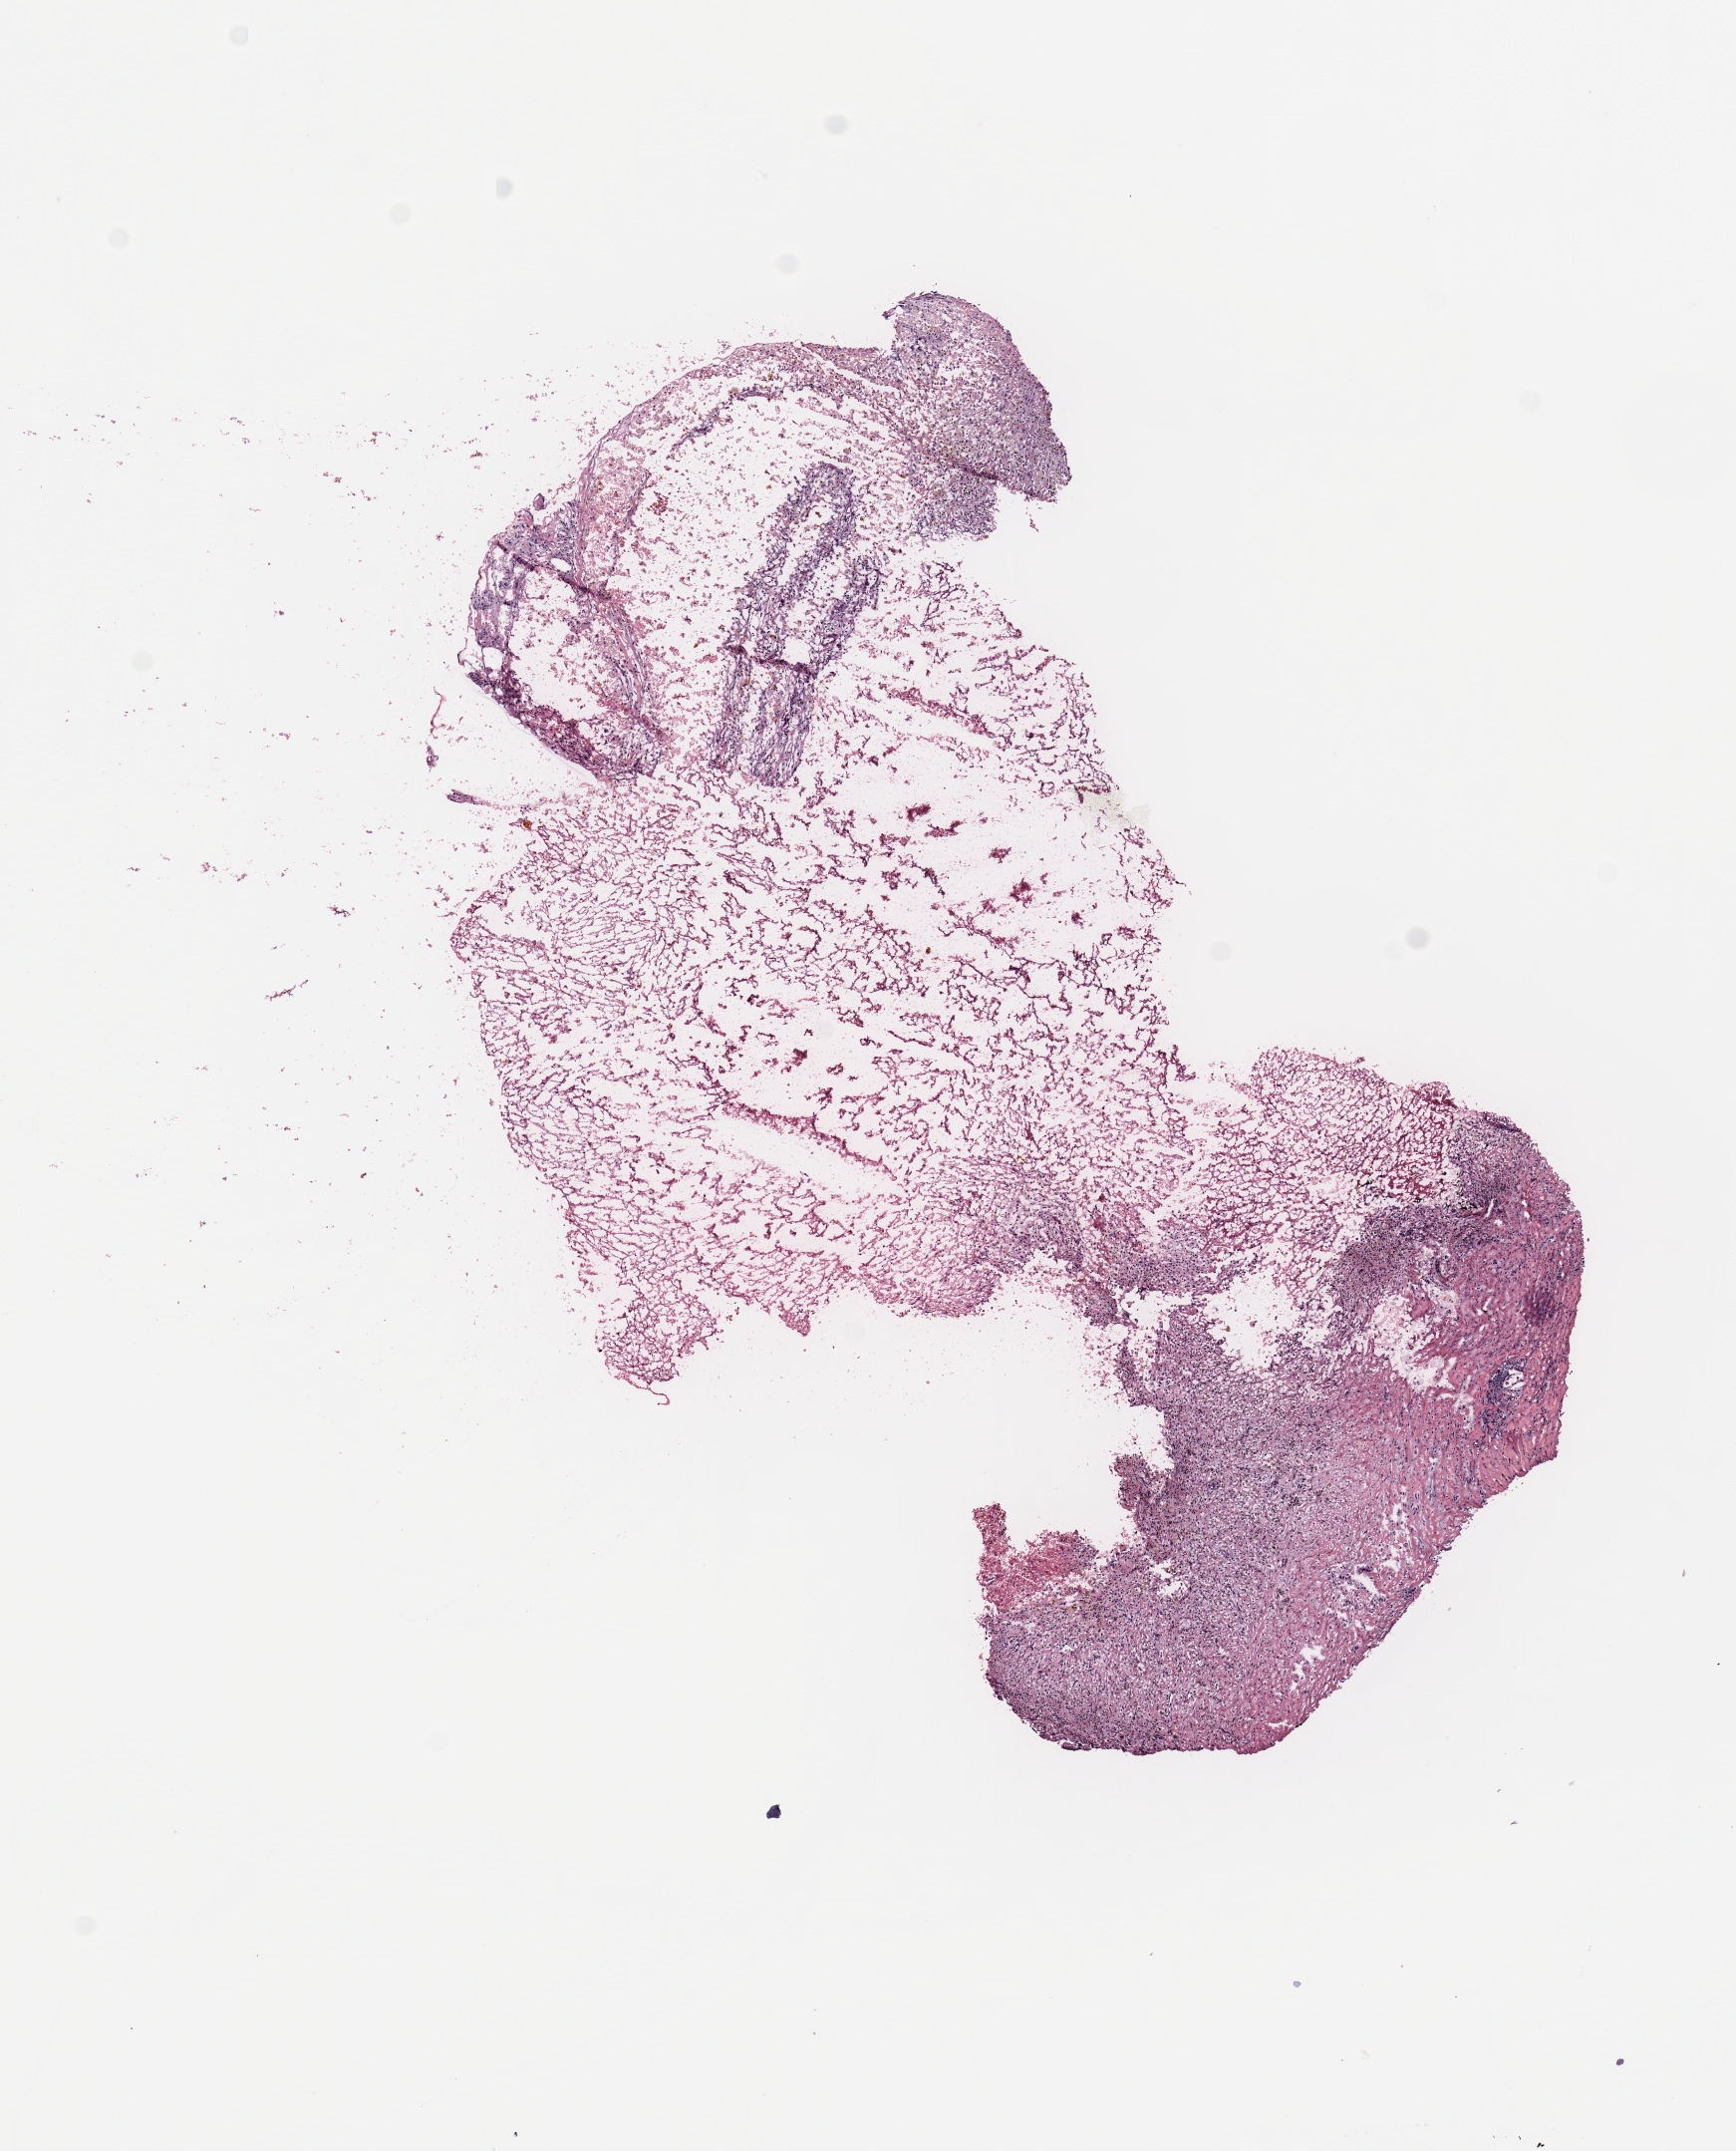
Digitized H&E-stained tissue section (whole slide), whole scanned area (about 6.9 x 8.5 mm, acquisition: 20x scan) shown as a low-resolution overview; breast, tissue type not recorded.
* patient diagnosis (cohort enrolment): breast cancer (breast)